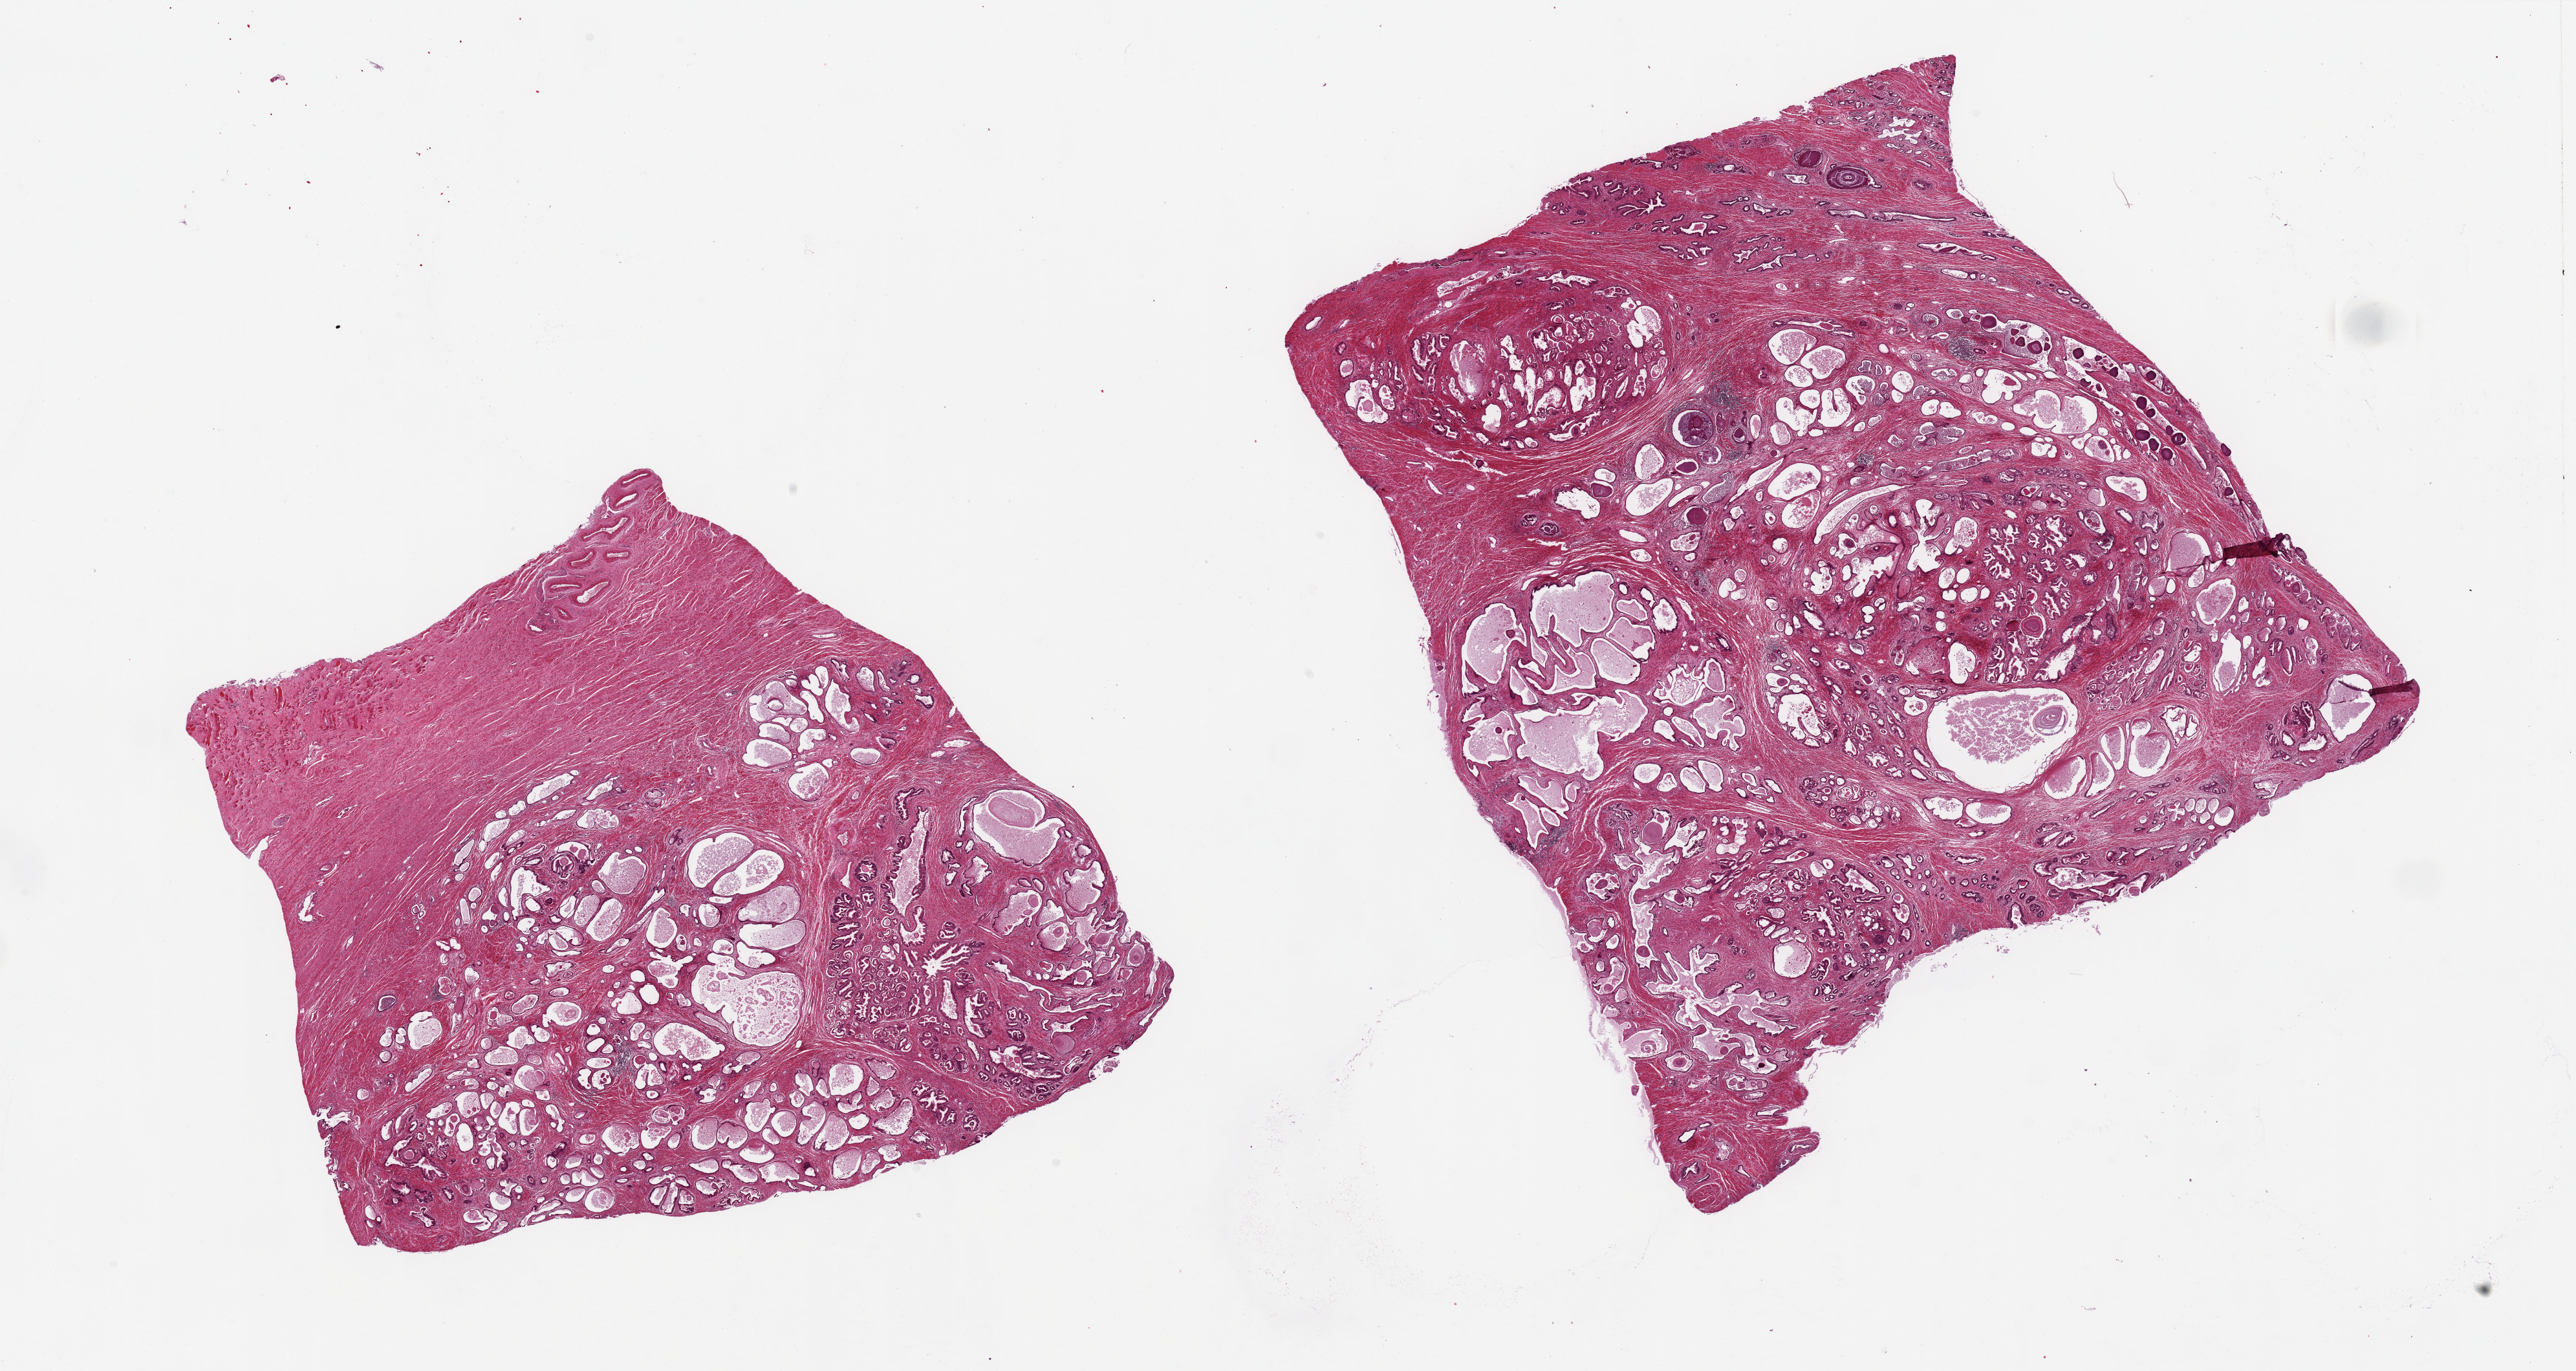
Haematoxylin and eosin whole-slide image, a low-resolution overview of the entire scanned area, about 31.5 x 16.8 mm (slide scanned at 20x), PAXgene-fixed, paraffin-embedded tissue, section of prostate (target tissue), tissue donor sample. Donor: male.
* review note (as recorded): 2 pieces 12x11 & 10x9 mm; nodular hyperplasia